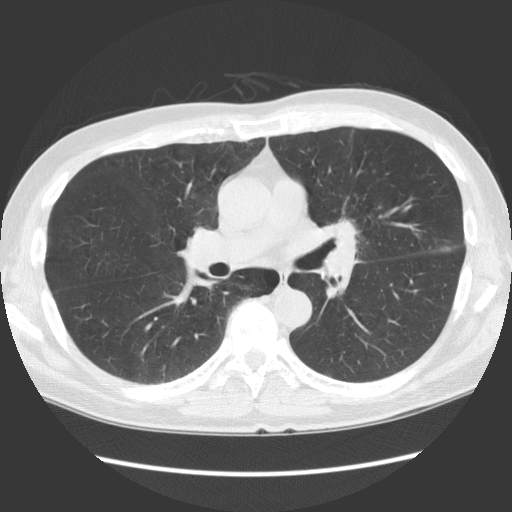
Low-dose screening chest CT, one axial slice; position 74 of 136 along the scan axis; reconstruction kernel STANDARD; 140 kVp; lung window (W 1500 / L -600 HU); 512 × 512 image matrix, field of view 360 × 360 mm.
Annotated regions visible in this slice (manually delineated by an expert):
- lesion 1 (tumor, hilum of left lung): bounding box (x1, y1, x2, y2) in pixels: (328, 218, 358, 256)